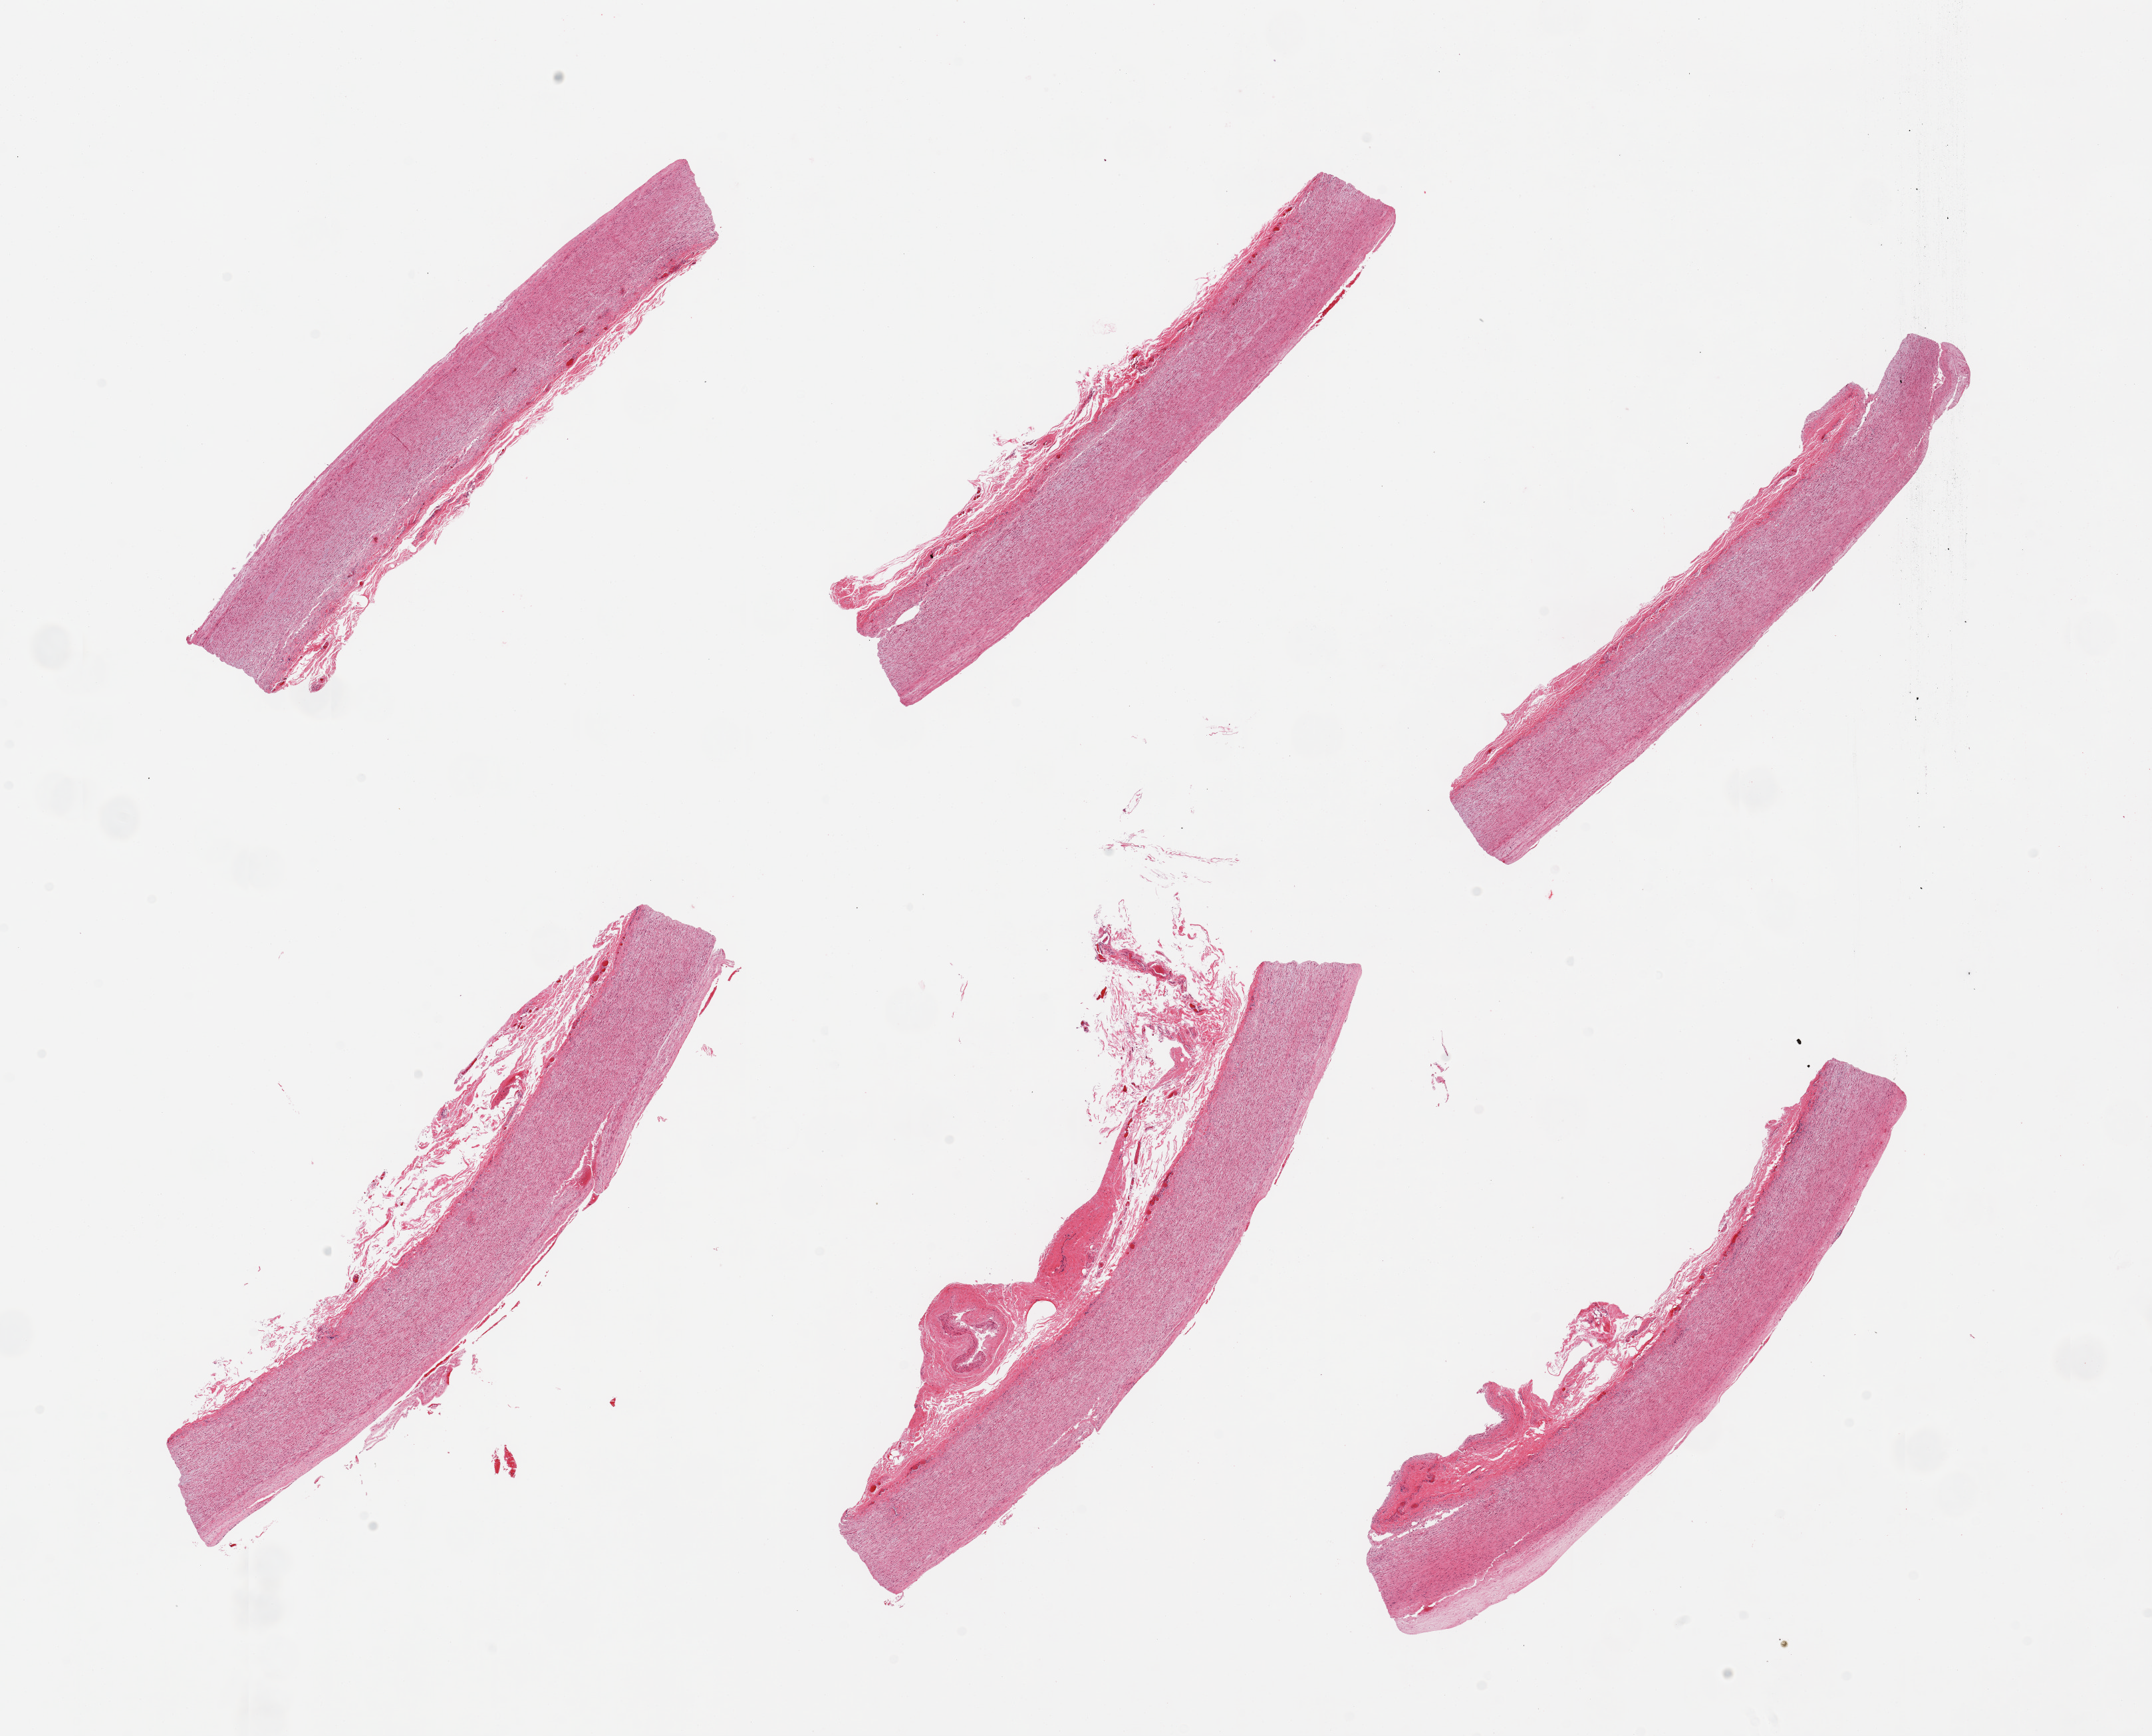
Digitized hematoxylin and eosin (H&E)-stained section, a low-resolution overview of the entire scanned area, about 25.6 x 20.6 mm, PAXgene-fixed, paraffin-embedded tissue, target tissue: aorta, donor tissue sample.
Reviewer comment on this tissue sample: 6 pieces, focal atherosis up to ~0.3mm.